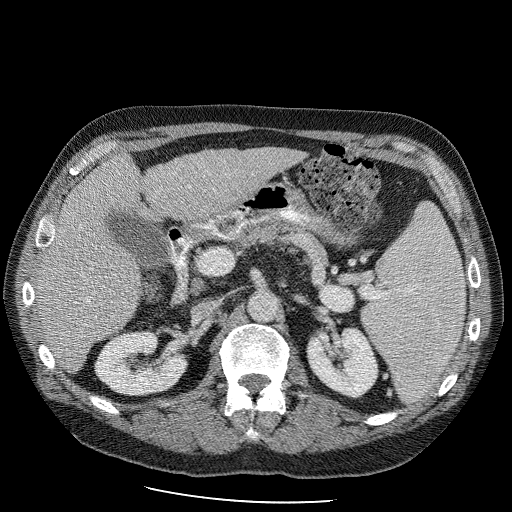
Contrast-enhanced abdominal CT (liver protocol), one axial slice; position 46 of 98 along the scan axis; 120 kVp; soft-tissue window (W 400 / L 40 HU); 512 × 512 image matrix, field of view 400 × 400 mm. From the clinical record (not read from this slice): diagnosis: hepatocellular carcinoma (patient treated with transarterial chemoembolisation; whether this scan precedes or follows treatment is not stated here); TNM stage (as recorded): Stage-II; Child-Pugh class: B; tumour differentiation: moderately differentiated; tumour nodularity: uninodular.
Outlined on this slice (semi-automatic segmentation, software-assisted and operator-edited):
- liver parenchyma outside the tumour (the mass and vessels are separate outlines, so this box may not span the whole liver): bounding box (x1, y1, x2, y2) in pixels: (34, 146, 302, 372)
- liver vessels: (46, 233, 90, 304)